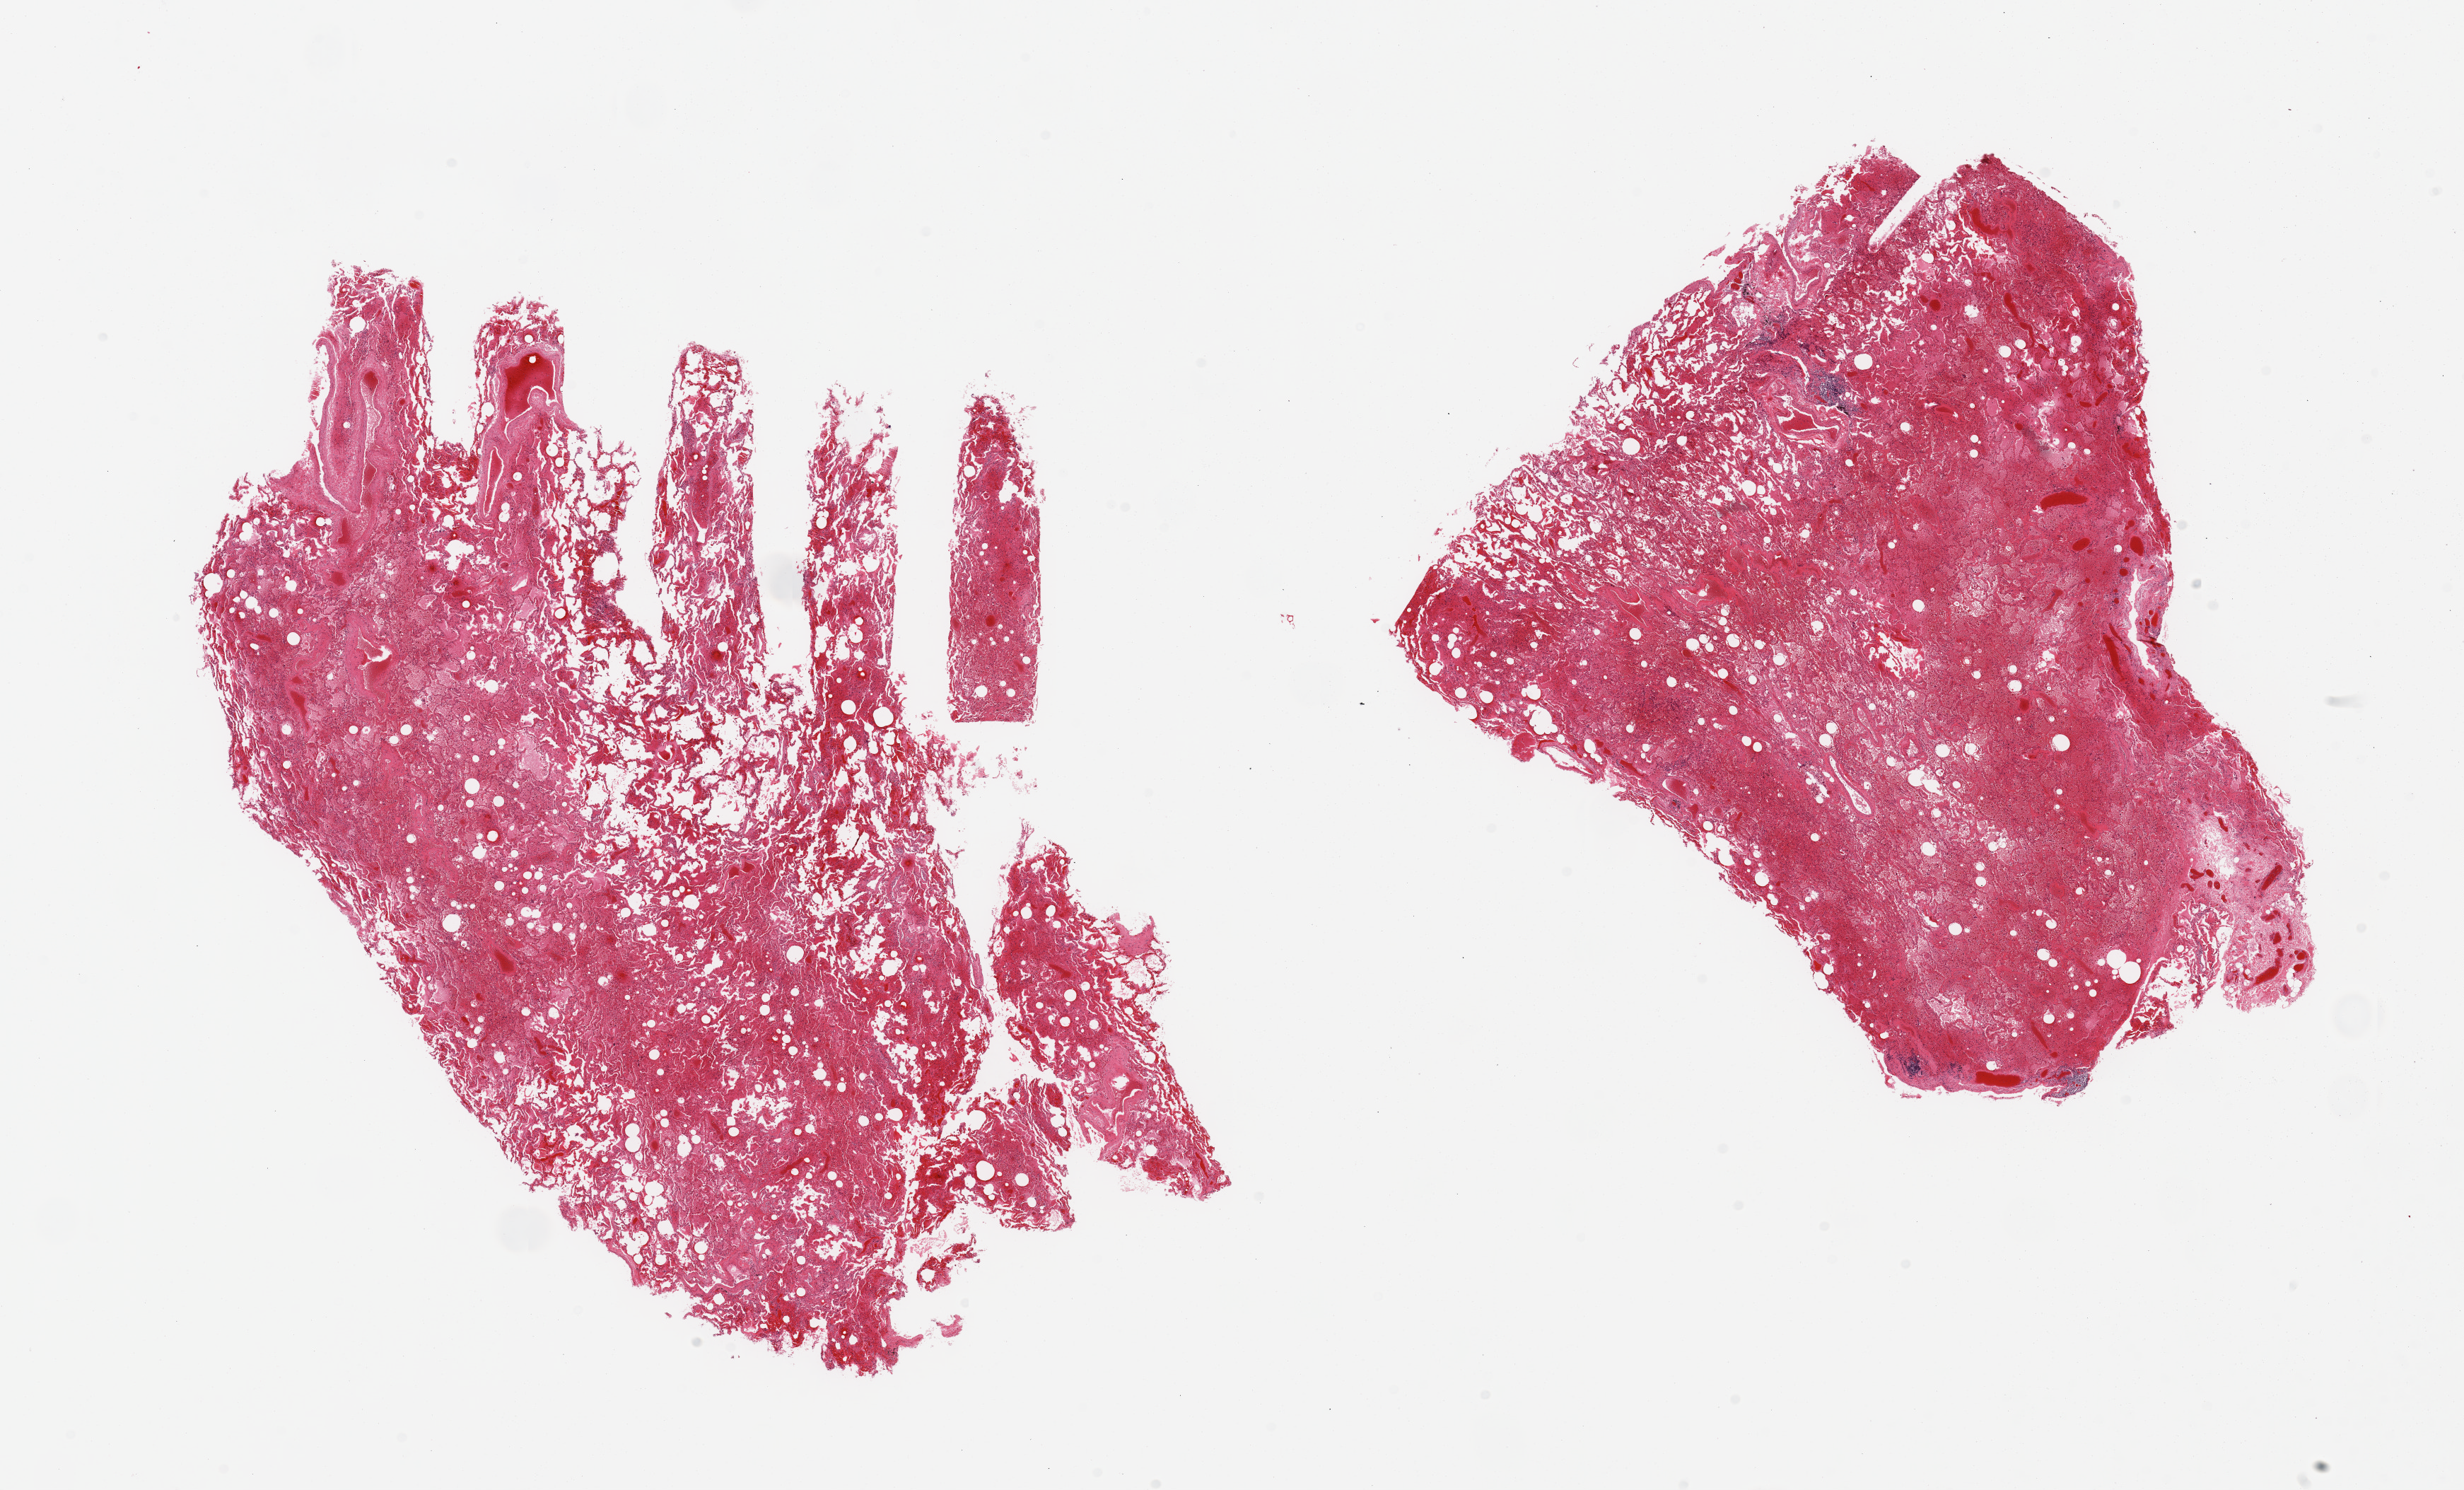
Whole-slide image, H&E stain — whole scanned area (about 27.6 x 16.7 mm, slide scanned at 20x) shown as a low-resolution overview; PAXgene-fixed, paraffin-embedded tissue; sampled site (target tissue): lung; tissue donor sample. Donor sex: male.
* reviewer comment on this tissue sample: 2 pieces; severe congestion, edema and hemorrhage